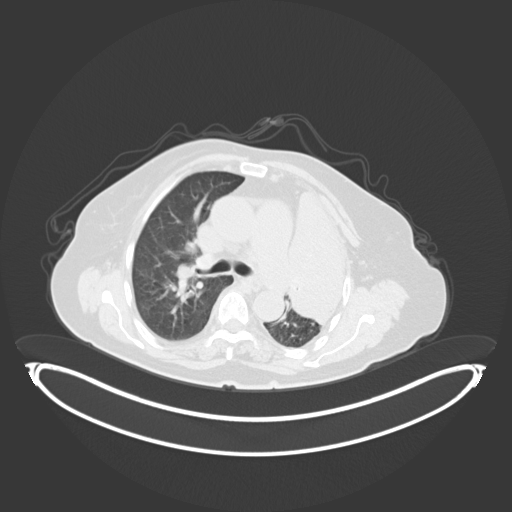
Chest CT, one axial slice; slice 209 of 284 in the series (ordered by position); 120 kVp; lung window (W 1500 / L -600 HU); 3 mm slice thickness; 512 × 512 image matrix, field of view 500 × 500 mm. Female patient, age 75 years. From the clinical record (not read from this slice): clinical TNM (as recorded): T3 N3 M1.
Outlined on this slice (bounding box drawn by a radiologist):
- lung tumour (recorded histology: adenocarcinoma): bounding box [x1, y1, x2, y2] px = [282, 186, 348, 332]